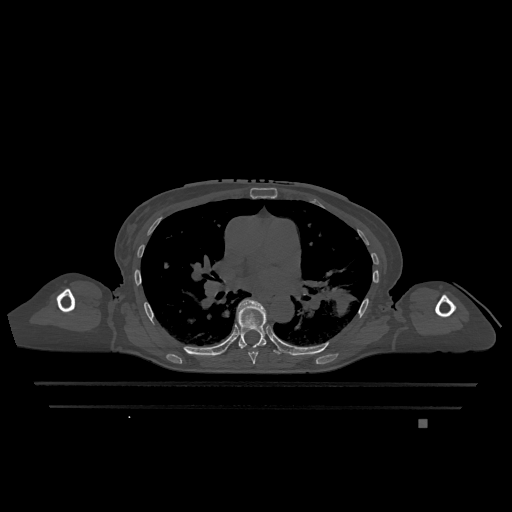
CT including the spine, one axial slice; slice 761 of 1317 in the series (ordered by position); bone window (W 1800 / L 400 HU); 512 × 512 image matrix, field of view 500 × 500 mm. Patient: female, 74 years. From the clinical record (not read from this slice): primary cancer: lung; vertebrae with lytic lesions (as recorded): T1, T4, T5, T6, L4, L5.
Outlined on this slice (semi-automatically segmented with operator editing):
- T6 vertebra: box from (x=240, y=327) to (x=267, y=364) px
- T7 vertebra: (x=237, y=299)–(x=280, y=354)